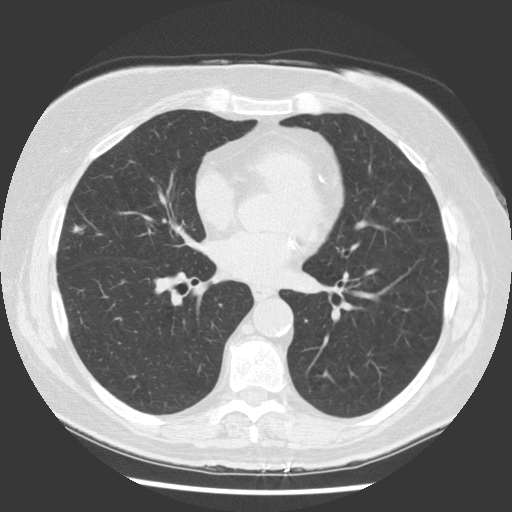
Chest CT (low-dose screening protocol), one axial image. First (baseline) screen. Lung window (W 1500 / L -600 HU). 2.5 mm slice thickness. Standard (soft-tissue) reconstruction kernel (STANDARD). Female, age 66 years at enrolment.
Expert-annotated lung lesion, box from (x=51, y=210) to (x=98, y=250) px. The screening reader recorded 2 non-calcified nodules or masses ≥4 mm on this exam; which of them this box marks is not recorded. Official screen result: positive, change unspecified: nodule(s) >= 4 mm or enlarging nodule(s), mass(es), or other non-specific abnormalities suspicious for lung cancer.